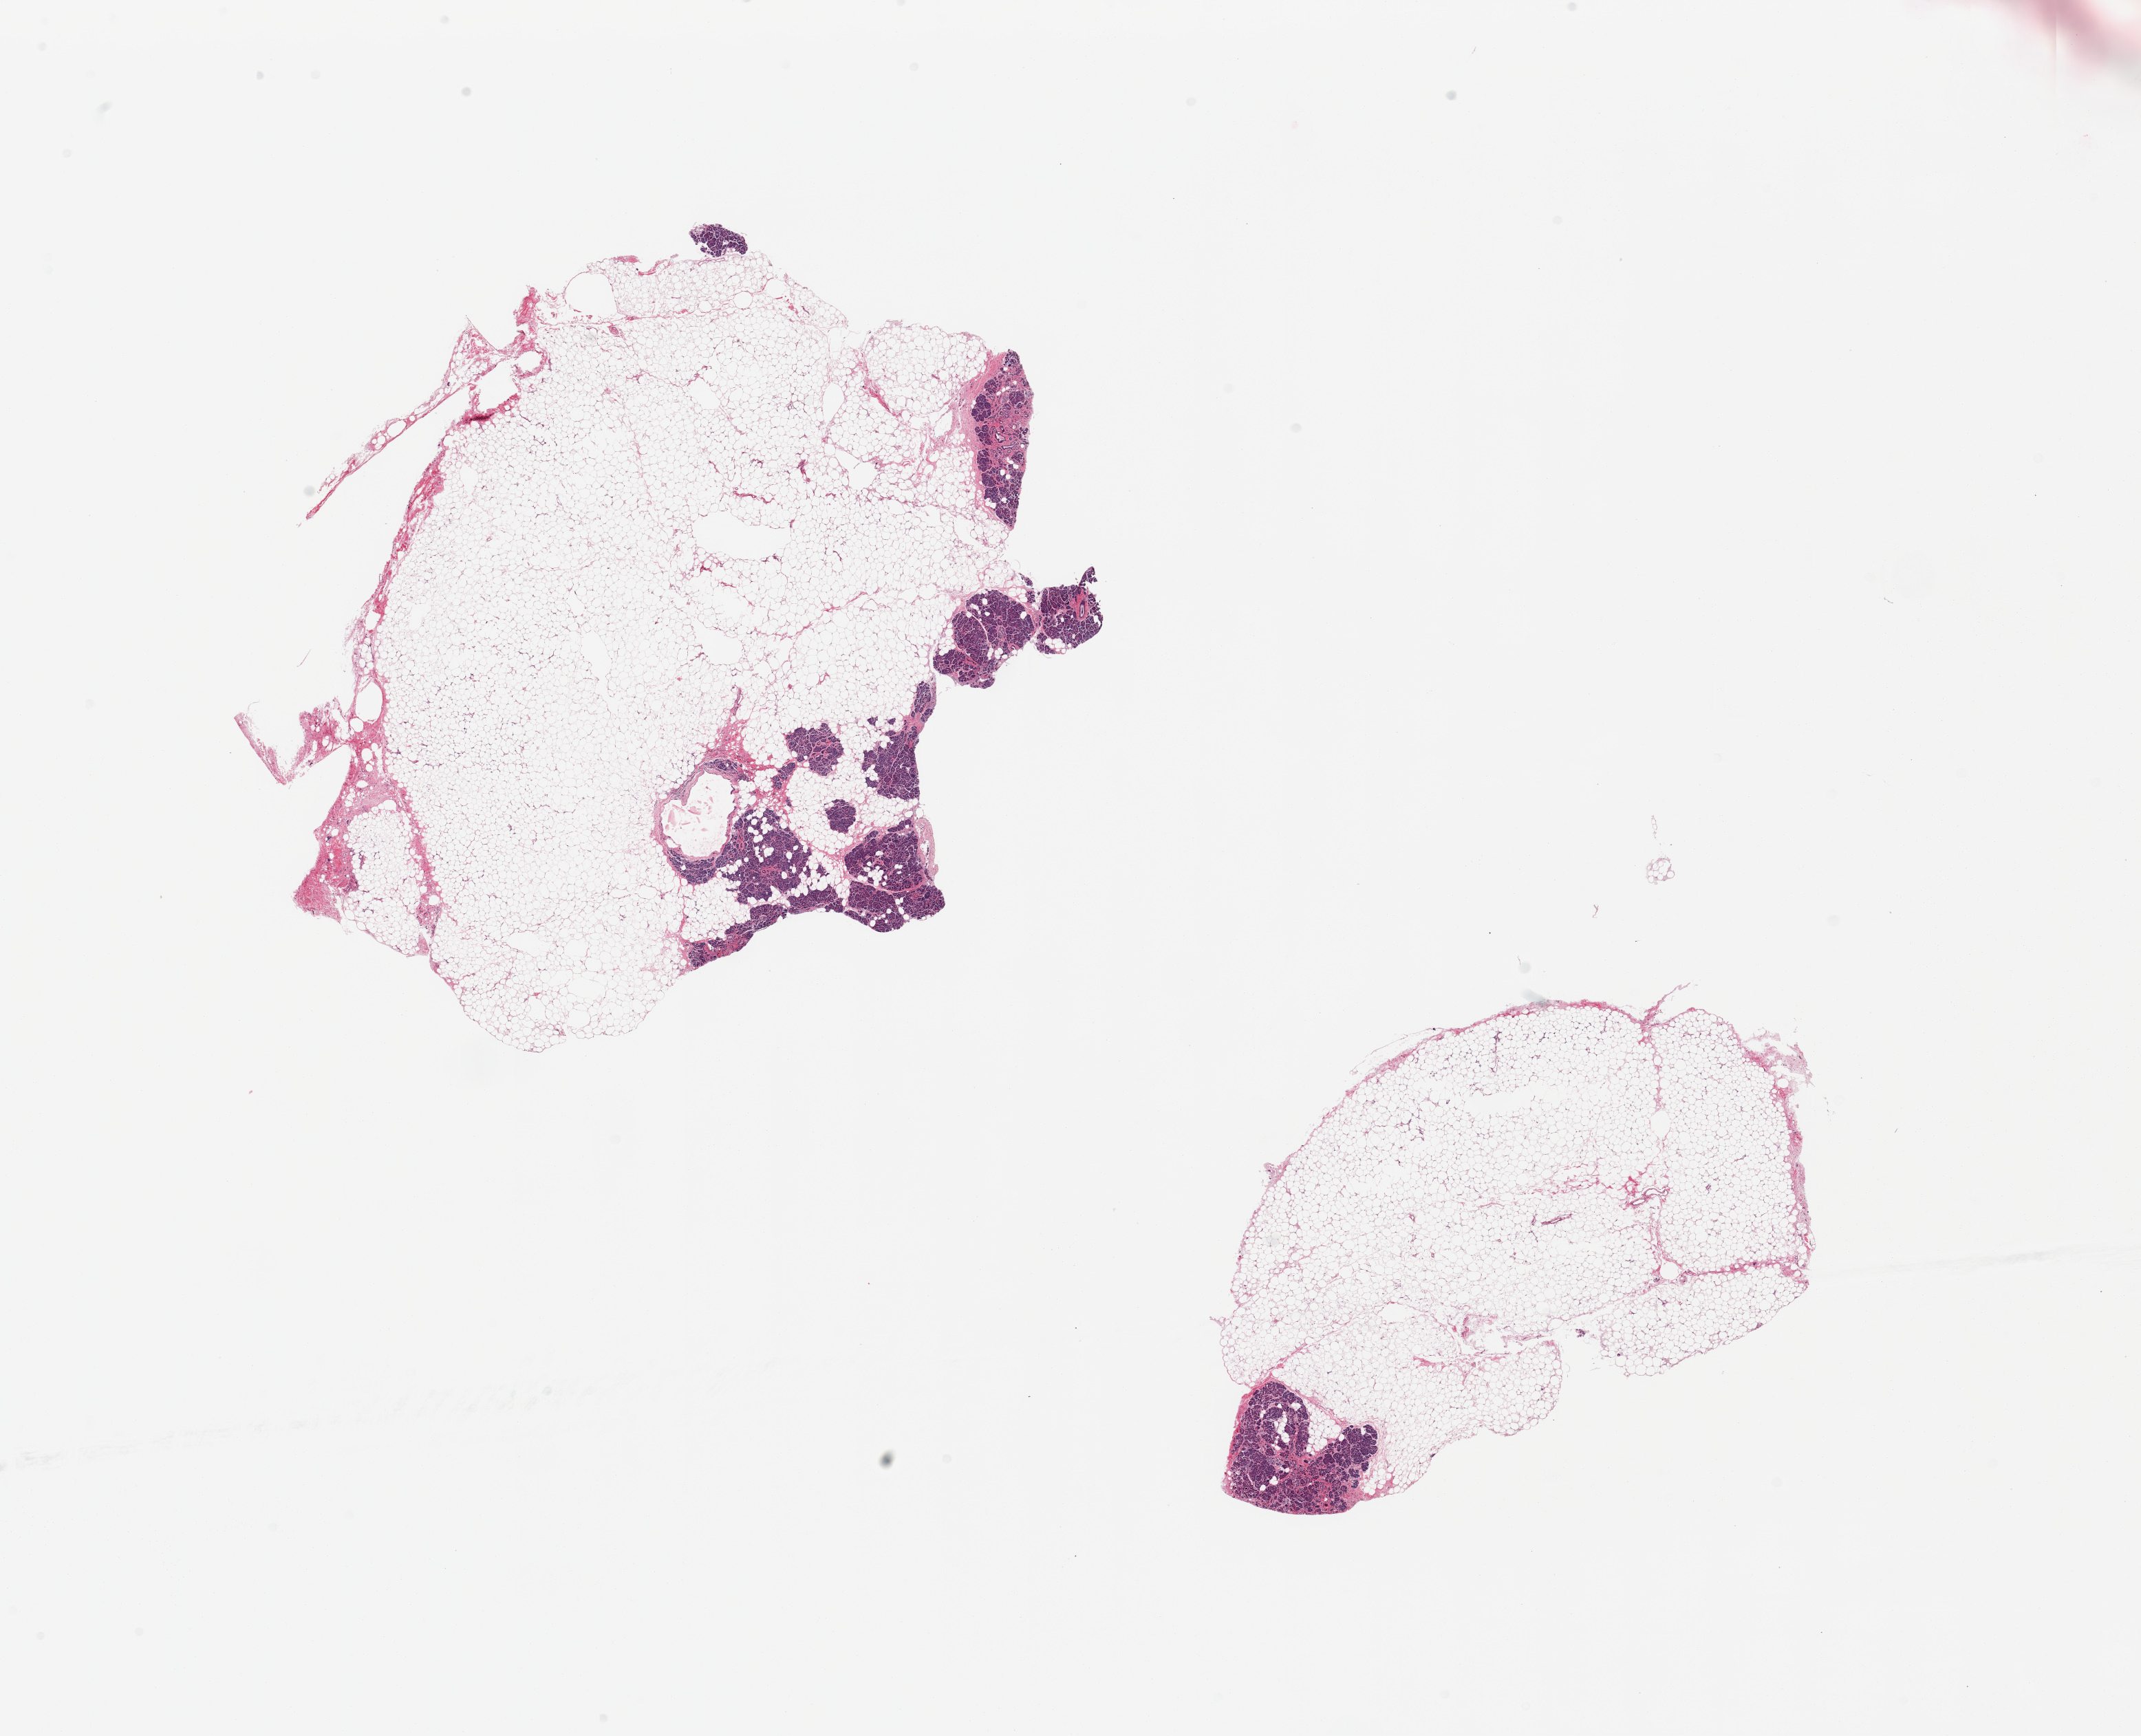
Whole-slide image, hematoxylin and eosin (H&E) stain — shown as a low-resolution overview of the whole scanned area (about 24.6 x 20.0 mm, from a 20x scan). PAXgene-fixed, paraffin-embedded tissue. Section of pancreas (target tissue). Donor tissue sample. Donor sex: male.
Pathologist's review note for this sample: 2 pieces, mainly fat, only ~10% pancreatic parenchyma.